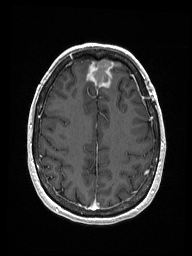
Brain MRI from a brain-tumour surgery series, one axial slice. Slice 52 of 192 in the series (ordered by position). T1-weighted post-contrast. 1 mm slice thickness. 192 × 256 image matrix. From the clinical record (not read from this slice): histopathology: Metastastic Carcinoma from Breast primary.
Annotated regions visible in this slice (manually delineated by an expert):
- previous resection cavity: bounding box [x1, y1, x2, y2] px = [92, 60, 115, 85]